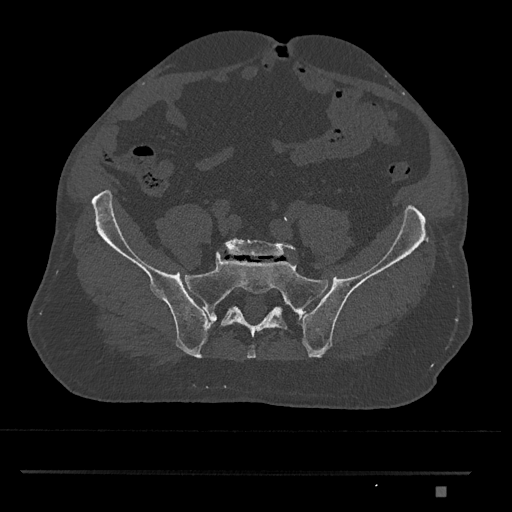
CT including the spine, one axial slice; position 503 of 1134 along the scan axis; bone window (W 1800 / L 400 HU); 512 × 512 image matrix. Male patient, age 65 years. From the clinical record (not read from this slice): primary cancer: prostate.
Structures marked on this image (semi-automatically segmented with operator editing):
- L5 vertebra: bounding box [x1, y1, x2, y2] px = [224, 238, 296, 258]